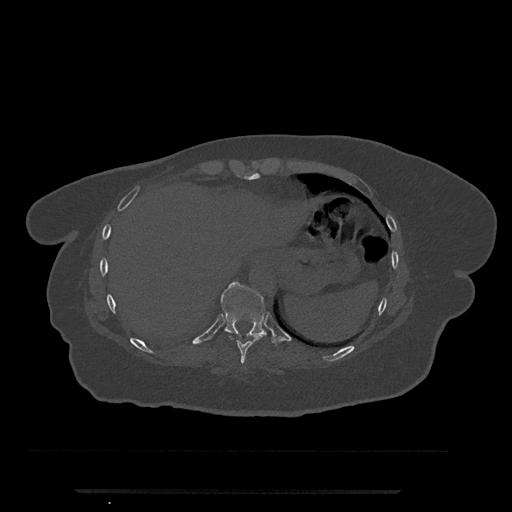
CT including the spine, one axial slice. Slice 311 of 797 in the series (ordered by position). Reconstruction kernel Br40s/3. 120 kVp. Bone window (W 1800 / L 400 HU). 0.5 mm slice thickness. 512 × 512 image matrix, field of view 440 × 440 mm. Female patient, age 51 years. From the clinical record (not read from this slice): primary cancer: neuro; vertebrae with lytic lesions (as recorded): T8.
Outlined on this slice (semi-automatic segmentation, software-assisted and operator-edited):
- T10 vertebra: box from (x=221, y=282) to (x=276, y=345) px
- T9 vertebra: (x=229, y=336)–(x=263, y=363)